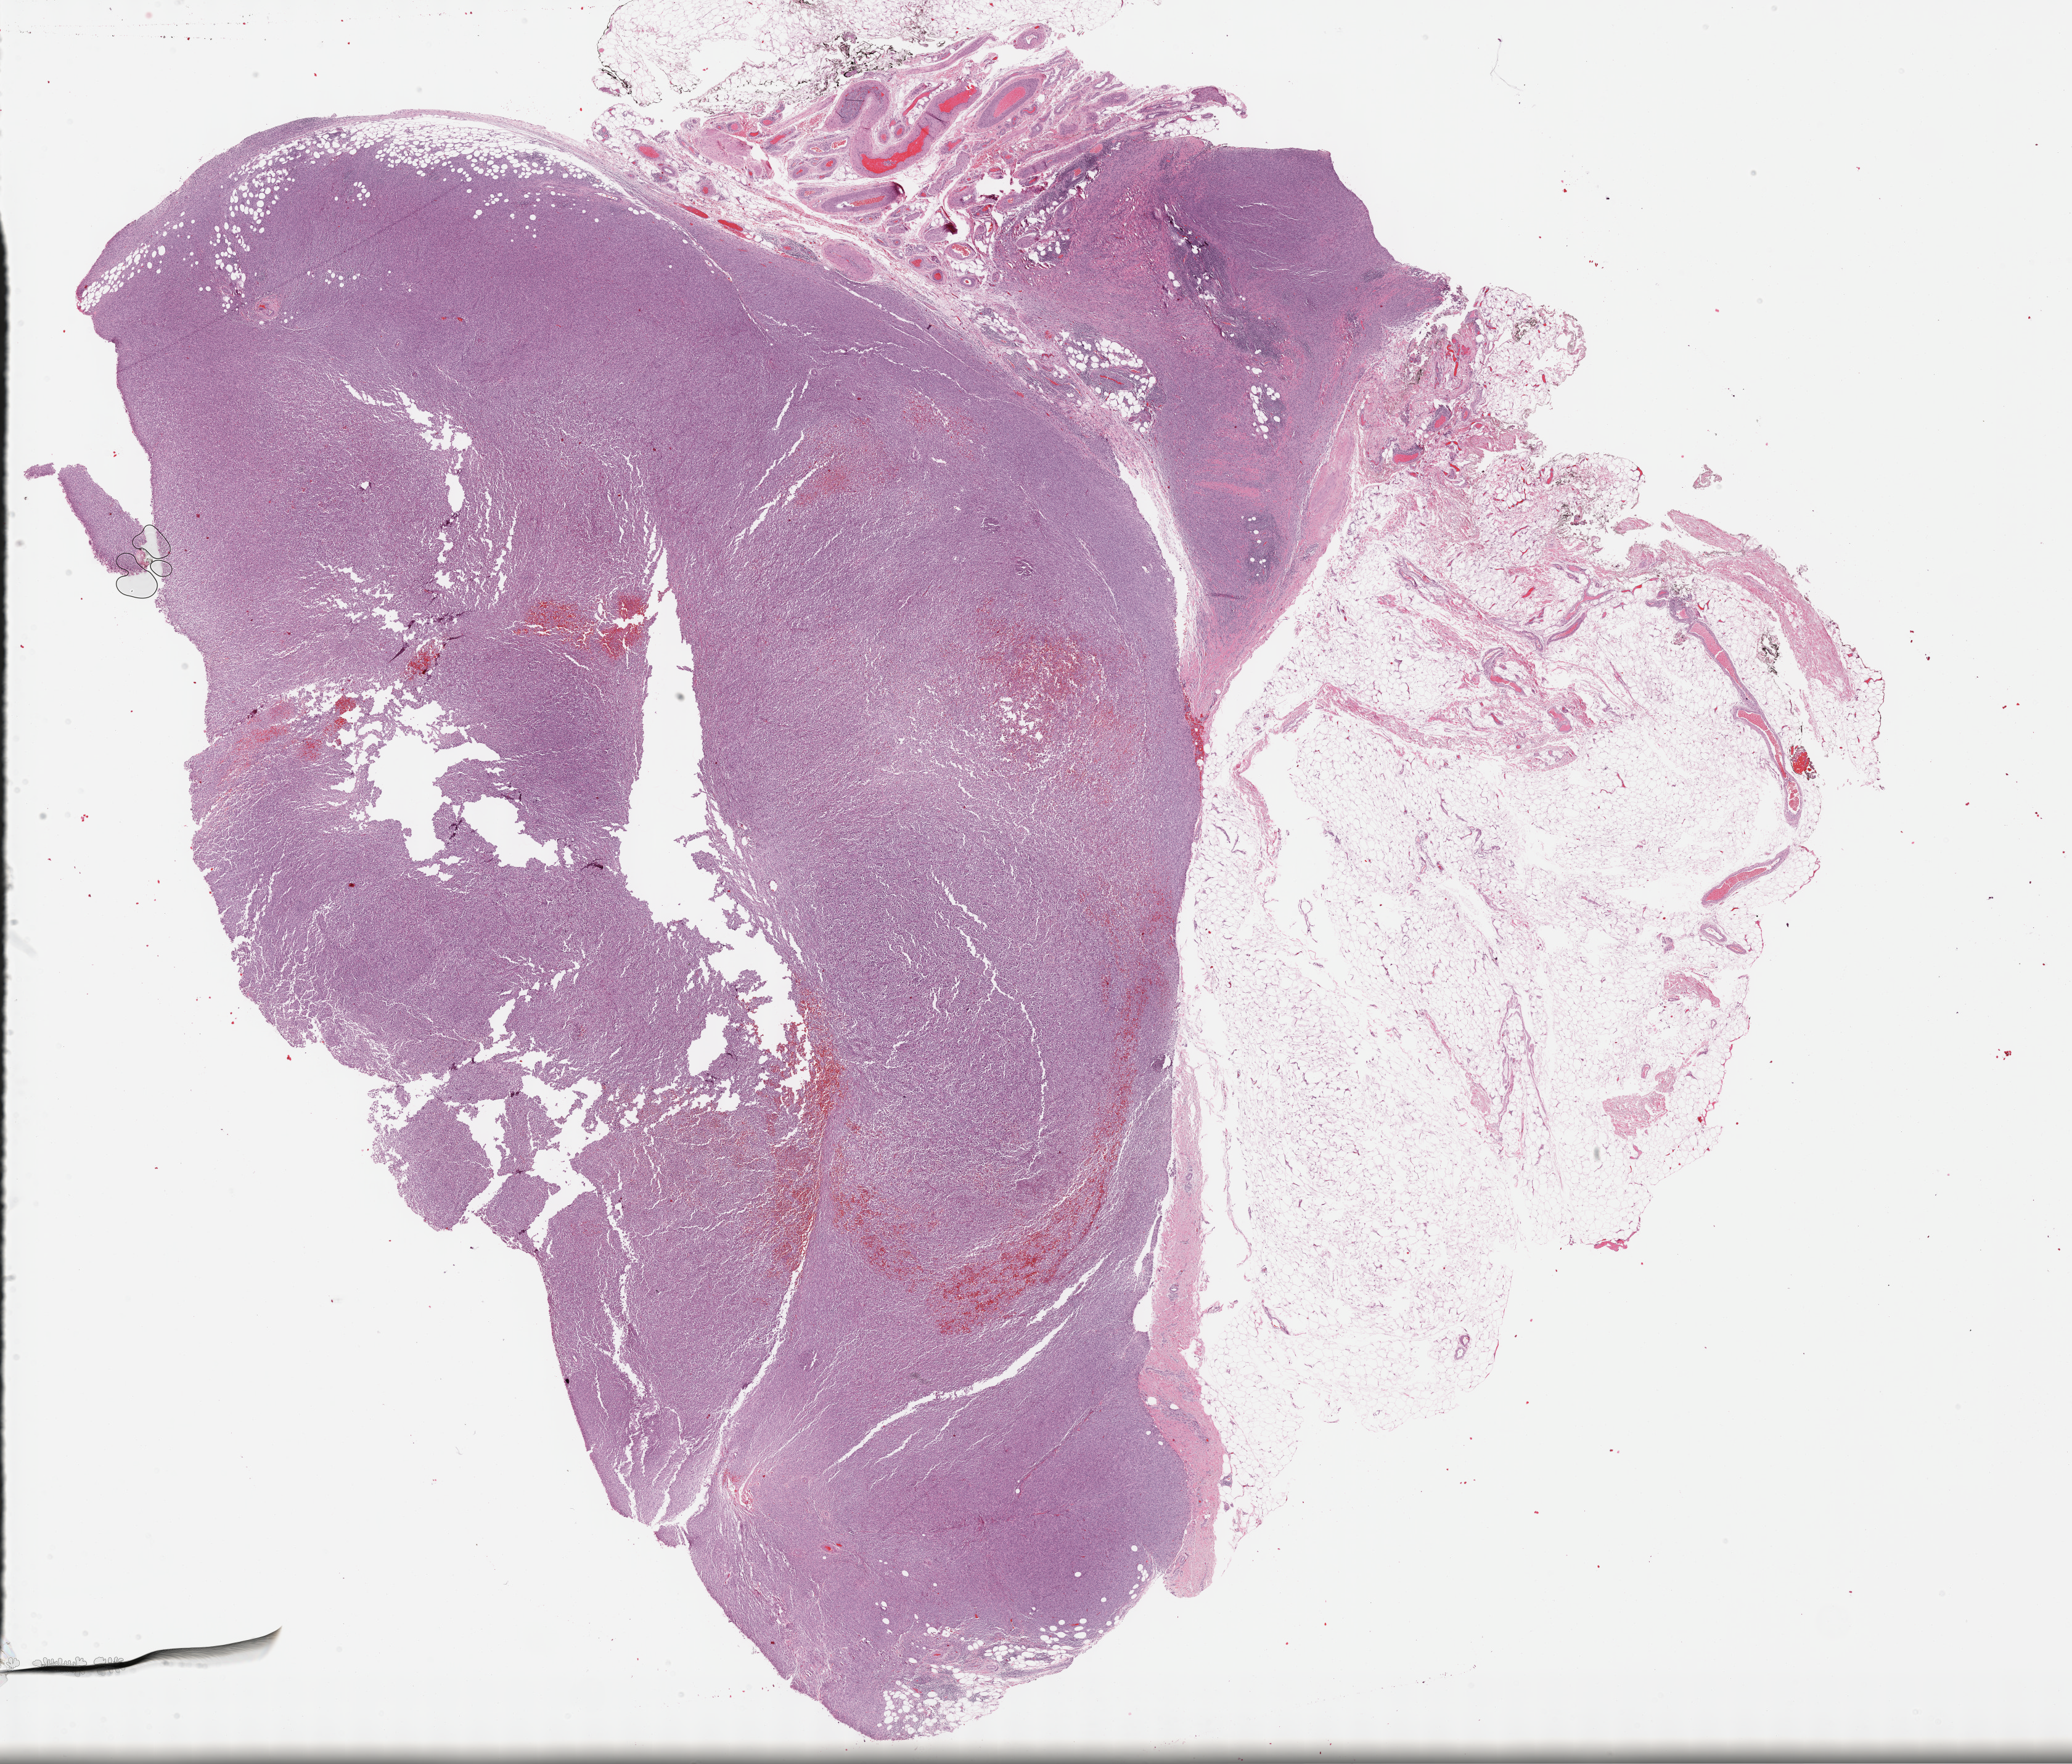
Whole-slide histology image, H&E-stained — shown as a low-resolution overview of the whole scanned area (about 27.2 x 23.1 mm, from a 40x scan), FFPE section, sample: primary tumour, retroperitoneum and peritoneum. Male, age 43 years at initial diagnosis.
* histologic diagnosis: Leiomyosarcoma, NOS